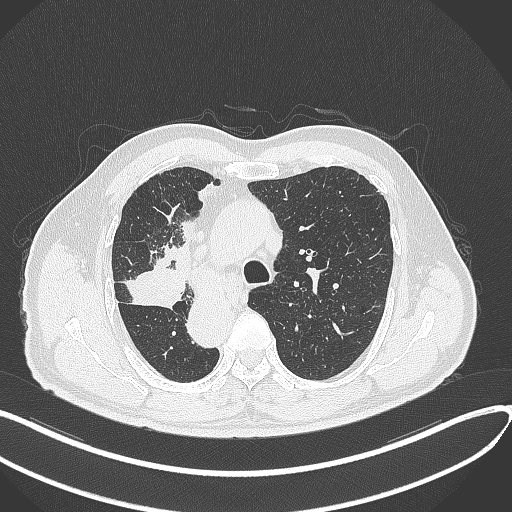
Chest CT, one axial slice; position 219 of 300 along the scan axis; reconstruction kernel B70f; 120 kVp; lung window (W 1500 / L -600 HU); 1 mm slice thickness; 512 × 512 image matrix, field of view 400 × 400 mm. Patient: male, 67 years. Case-level facts recorded for this patient, not image findings: clinical TNM (as recorded): T2a N0 M0.
Structures marked on this image (rectangle marked by the reading radiologist):
- lung tumour (recorded histology: squamous cell carcinoma): bounding box (x1, y1, x2, y2) in pixels: (123, 264, 186, 309)